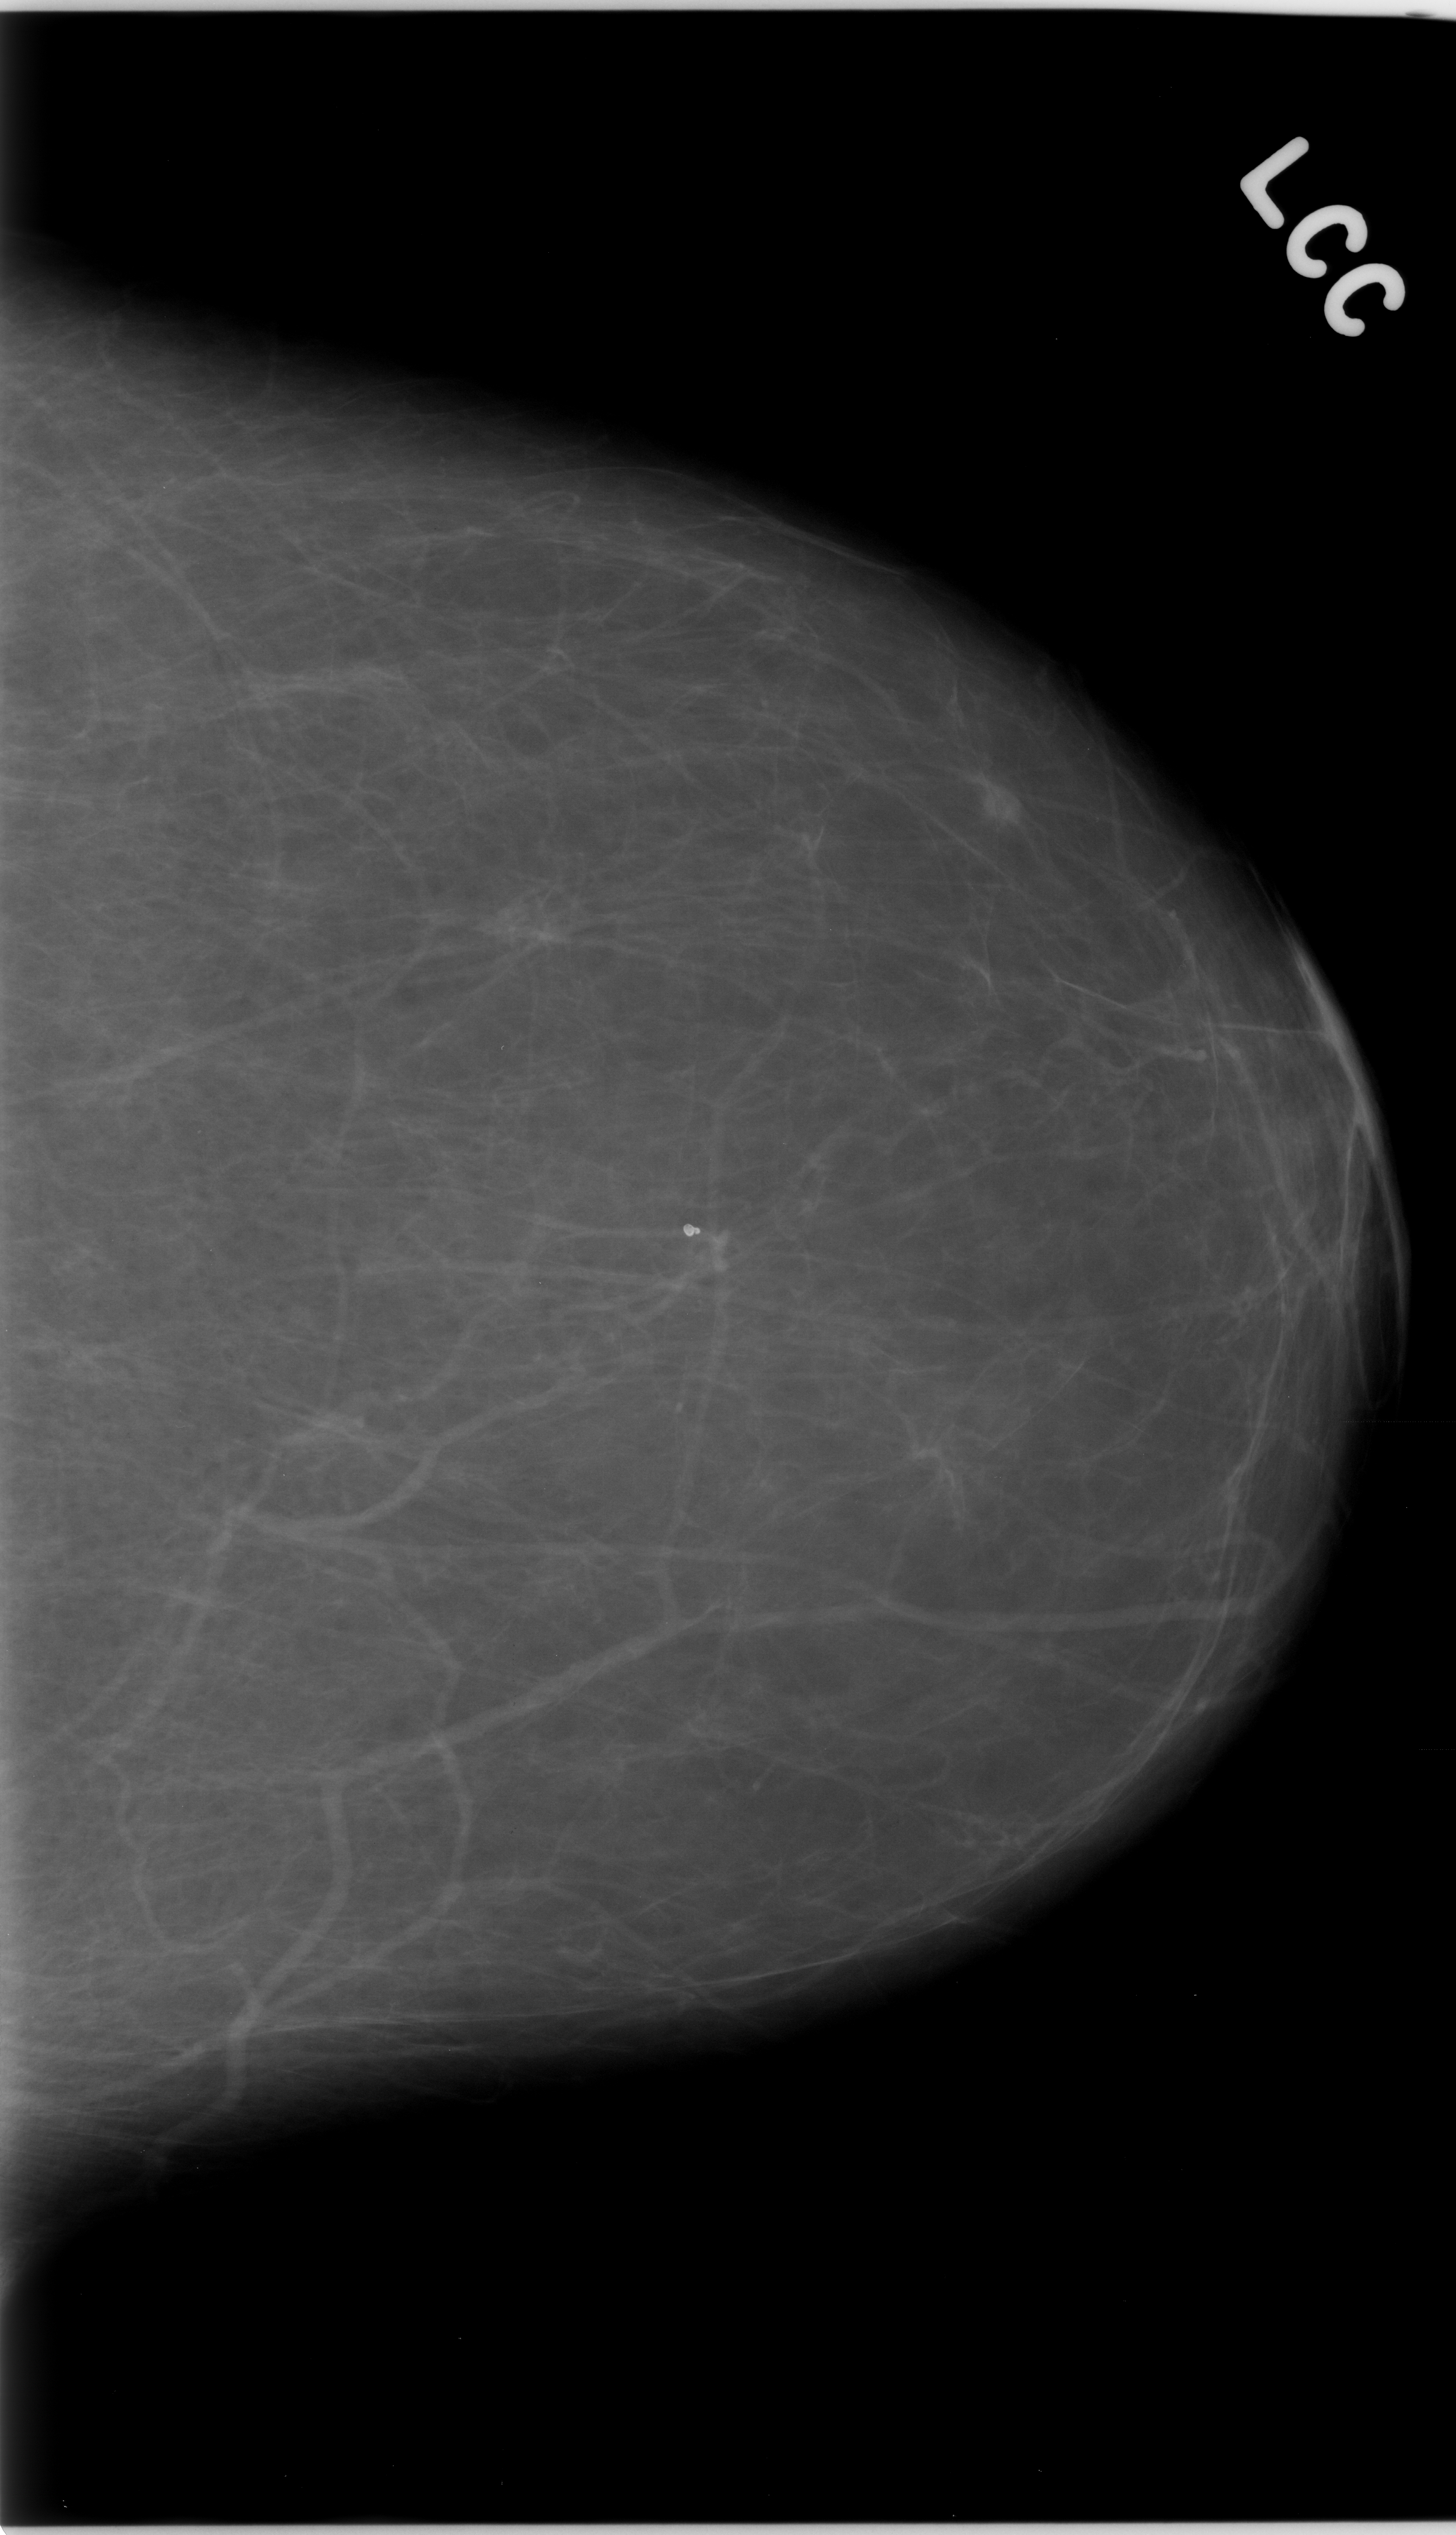
Scanned film-screen mammogram, left breast, craniocaudal (CC) view.
Abnormality record for this image: mass, shape oval, margins circumscribed; BI-RADS assessment category 4; pathology result (as recorded, not read from the image): malignant.